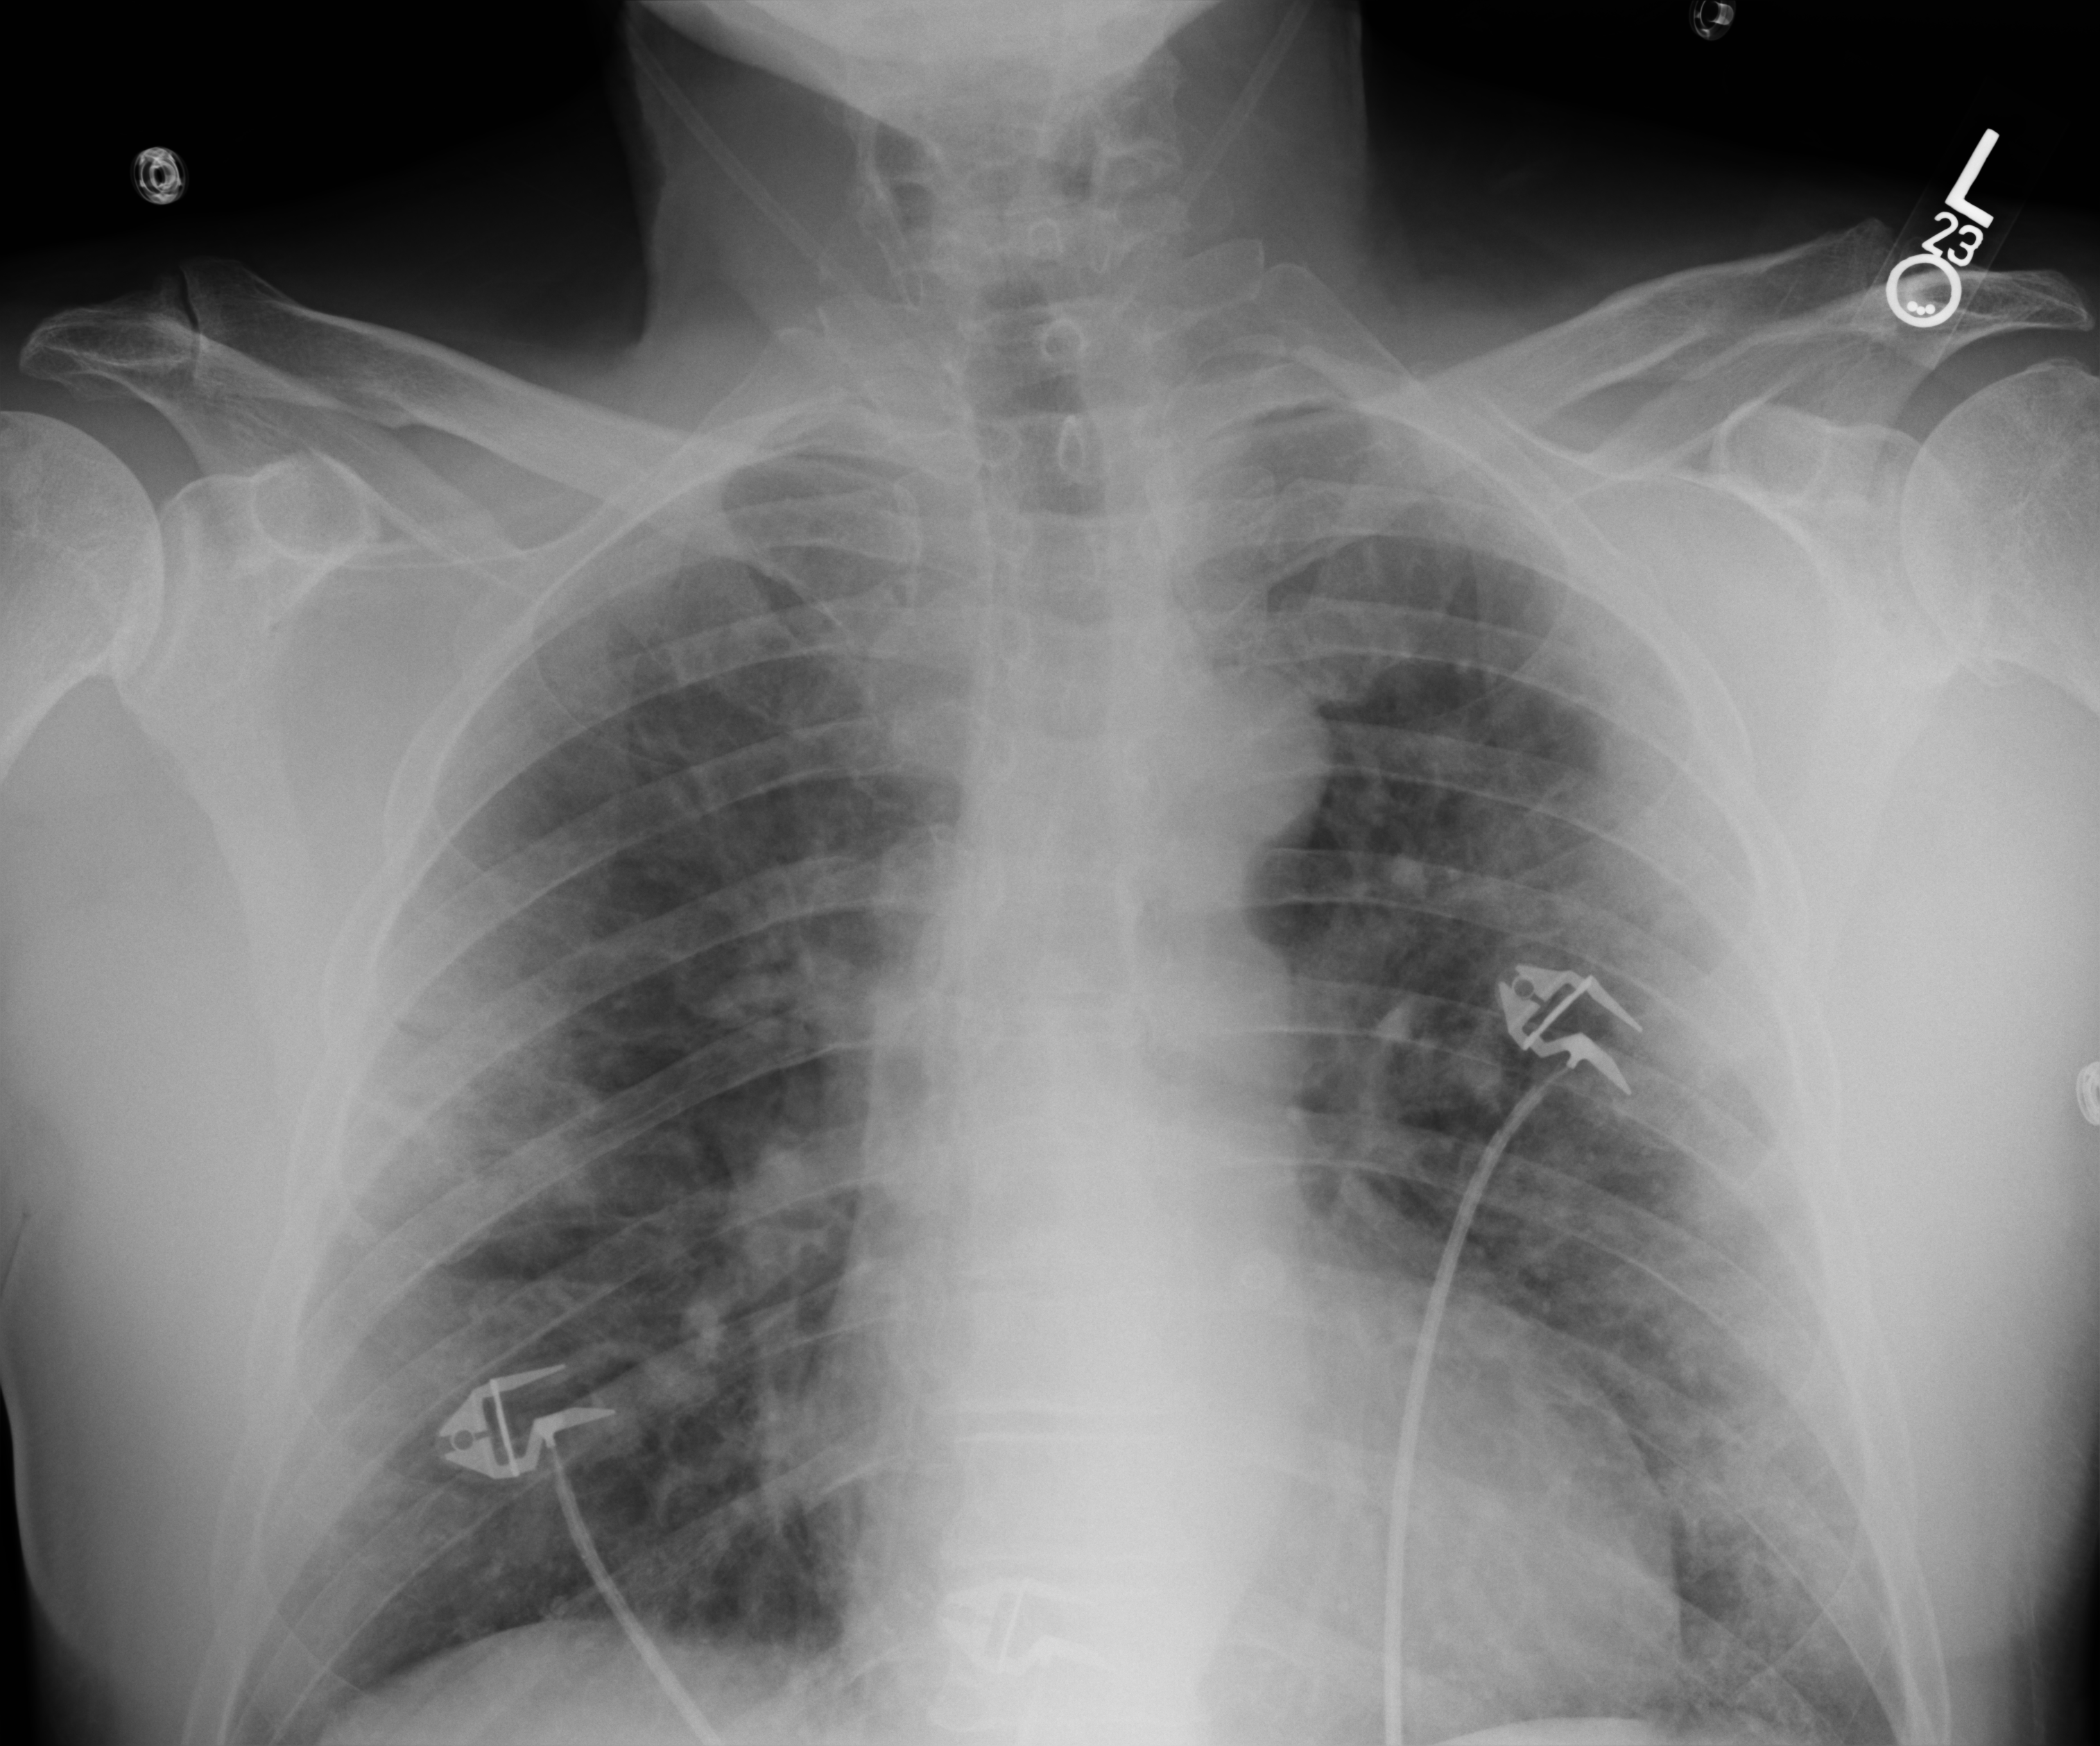
Chest X-ray (portable), anteroposterior (AP) projection. Male patient hospitalised with COVID-19, age 18–59 years.
From the hospital-stay record, not from the radiograph (when in the stay this image was taken is not recorded): admitted to intensive care during this hospital stay: no; length of hospital stay: 11 days.